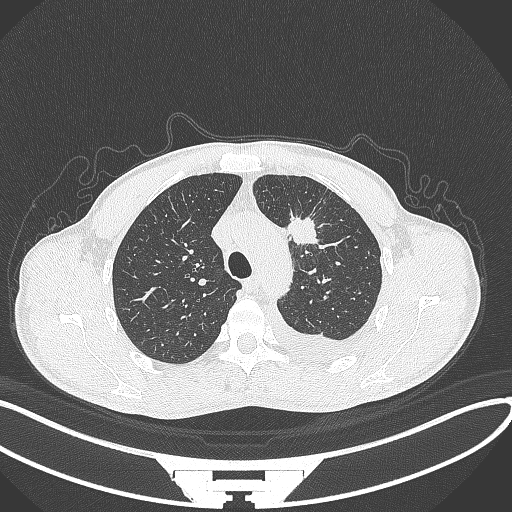
Chest CT, one axial slice. Position 255 of 371 along the scan axis. Reconstruction kernel B70f. Lung window (W 1500 / L -600 HU). 1 mm slice thickness. 512 × 512 image matrix, field of view 400 × 400 mm. Patient: male, 49 years. From the clinical record (not read from this slice): clinical TNM (as recorded): T1c N1 M1.
Annotated regions visible in this slice (rectangle marked by the reading radiologist):
- lung tumour (recorded histology: adenocarcinoma): box from (x=288, y=213) to (x=324, y=255) px